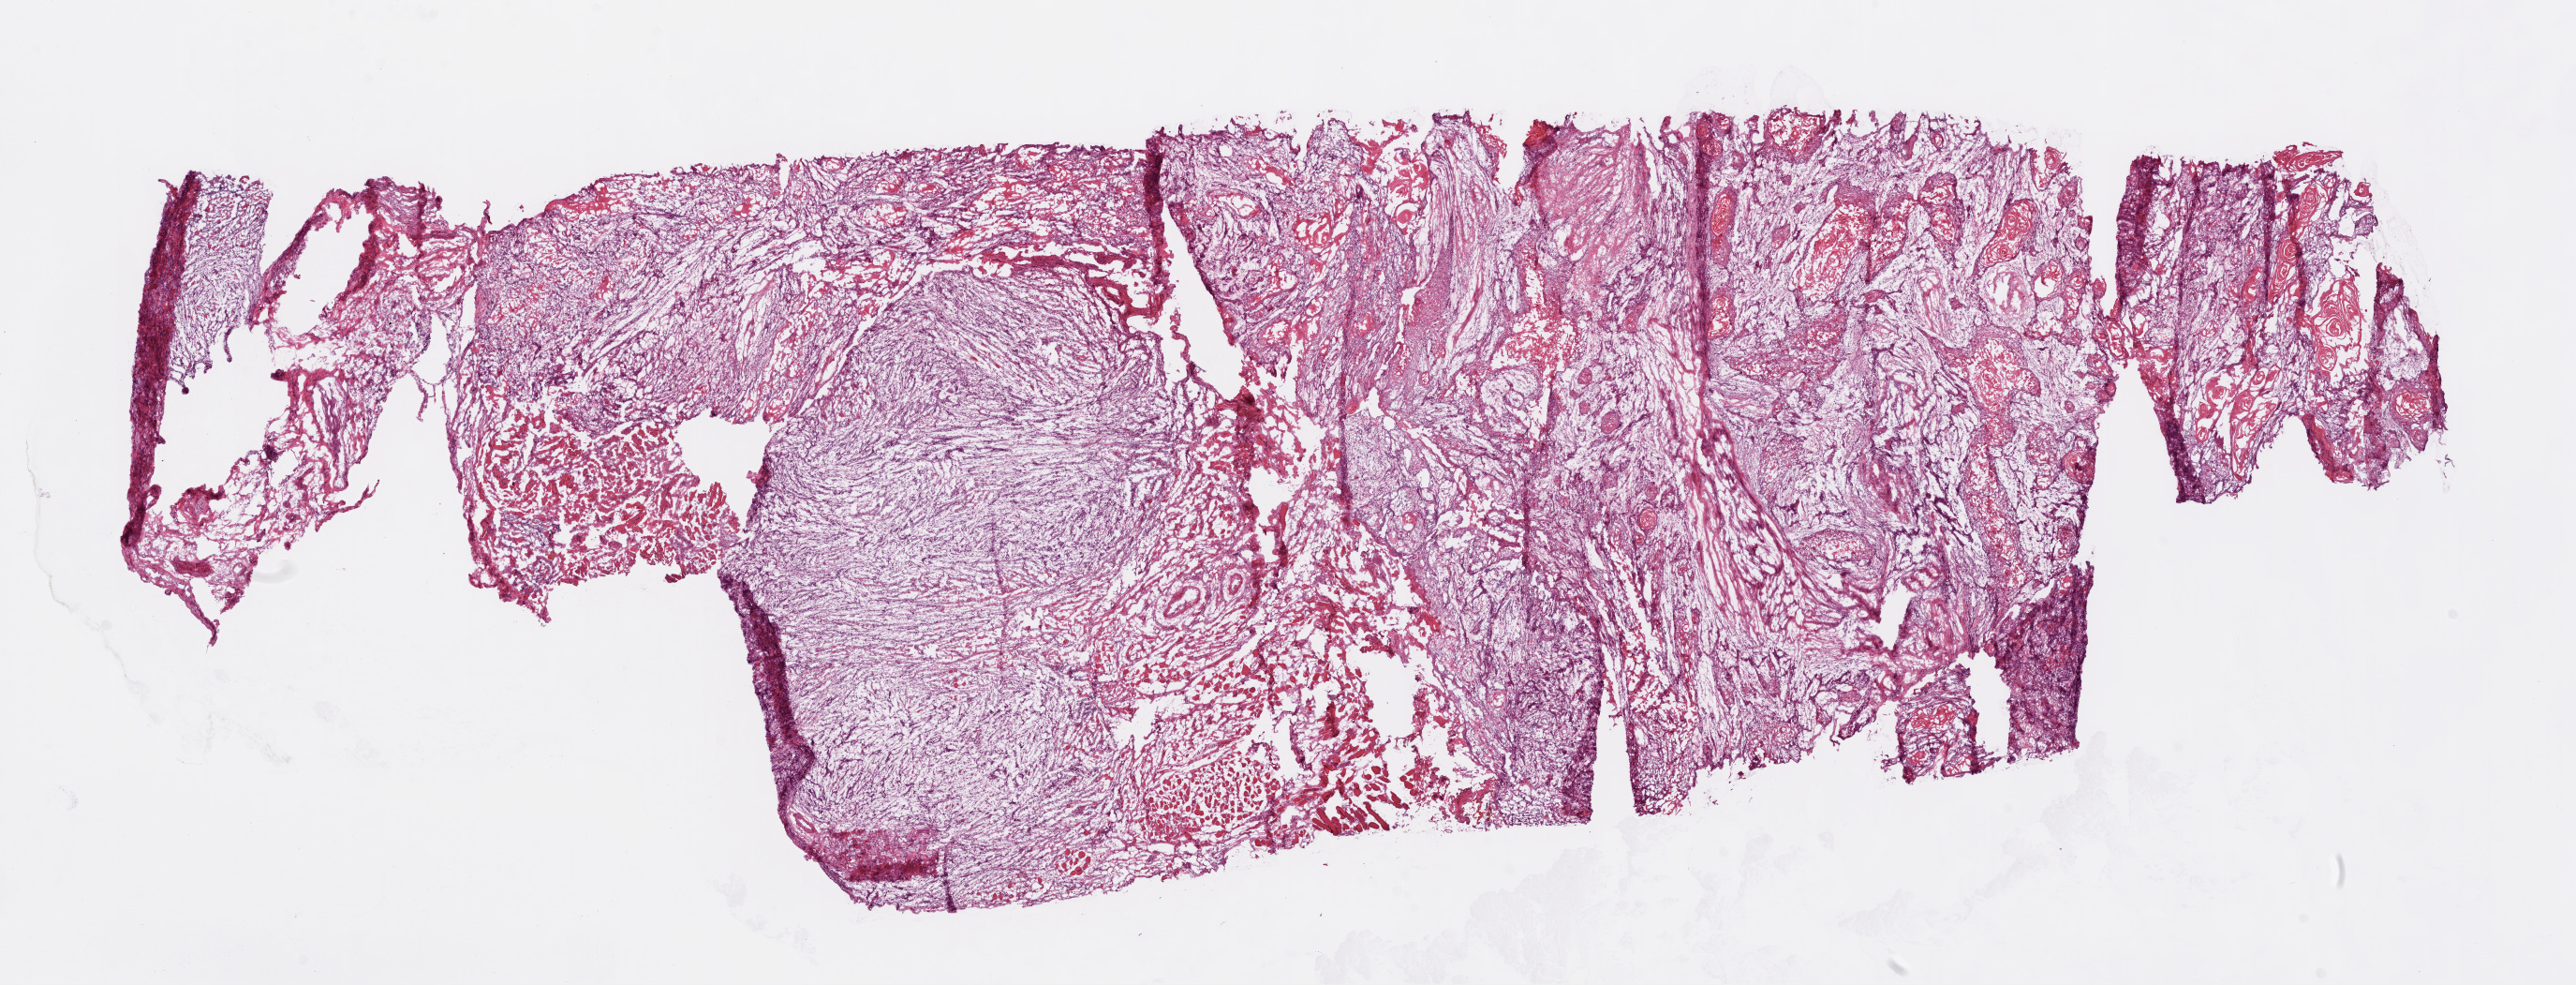
H&E-stained whole-slide image — low-resolution overview of the scanned area, about 22.1 x 8.4 mm, frozen section from the top of the tissue portion, head and neck, primary tumour sample. Patient: male, age at initial diagnosis 78 years. Histologic grade: G3 (poorly differentiated). Composition of this section per pathologist review: tumour cells 85%, tumour nuclei 80%, normal cells 0%, stromal cells 15%, necrosis 0%.
Diagnosis: Squamous cell carcinoma, NOS (tongue, NOS). AJCC pathologic stage: III.